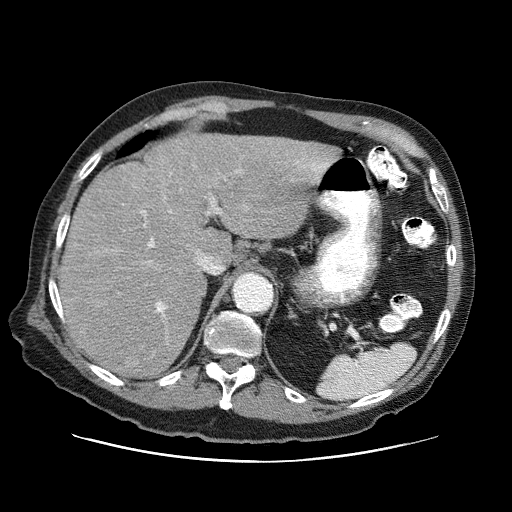
Contrast-enhanced abdominal CT (liver protocol), one axial slice. Position 51 of 87 along the scan axis. Reconstruction kernel STANDARD. One of 3 acquisitions stored at this slice position. Soft-tissue window (W 400 / L 40 HU). 2.5 mm slice thickness. 512 × 512 image matrix, field of view 400 × 400 mm. Case-level facts recorded for this patient, not image findings: diagnosis: hepatocellular carcinoma (patient treated with transarterial chemoembolisation; whether this scan precedes or follows treatment is not stated here); TNM stage (as recorded): Stage-IIIA; Child-Pugh class: A; tumour differentiation: well differentiated; tumour nodularity: multinodular.
Annotated regions visible in this slice (semi-automatically segmented with operator editing):
- abdominal aorta: bounding box (x1, y1, x2, y2) in pixels: (235, 273, 273, 311)
- liver parenchyma outside the tumour (the mass and vessels are separate outlines, so this box may not span the whole liver): (59, 134, 338, 376)
- liver vessels: (142, 163, 330, 317)